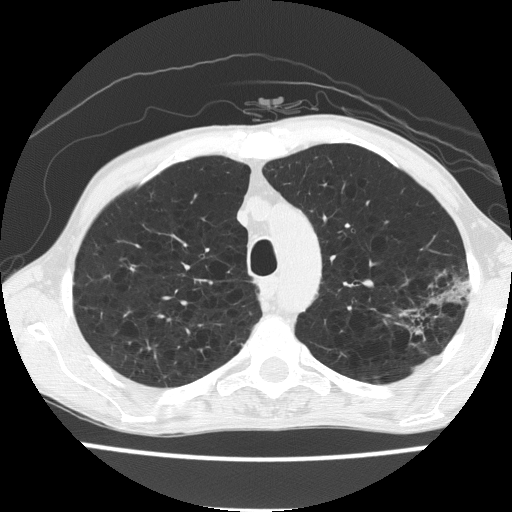
Low-dose screening chest CT, axial slice; baseline screening round; lung window (W 1500 / L -600 HU); lung (sharp) reconstruction kernel (FC51); slice 45 of 187 in the series; 512 × 512 image matrix. Male, age 60 years at enrolment. Current smoker at enrolment.
- Expert reader's lesion annotation, bounding box (x1, y1, x2, y2) in pixels: (392, 258, 473, 342).
- Screening reader's record for this exam: no non-calcified nodule ≥4 mm recorded.
- Lung cancer was diagnosed 490 days after this screen: bronchiolo-alveolar carcinoma, mucinous, left upper lobe, stage IV (AJCC 6th edition).